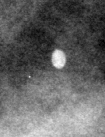
Cropped region of a digitized screen-film mammogram centred on a radiologist-marked abnormality, left breast, MLO view.
Calcifications, morphology round and regular; BI-RADS assessment category 2; benign without callback (not worked up further).